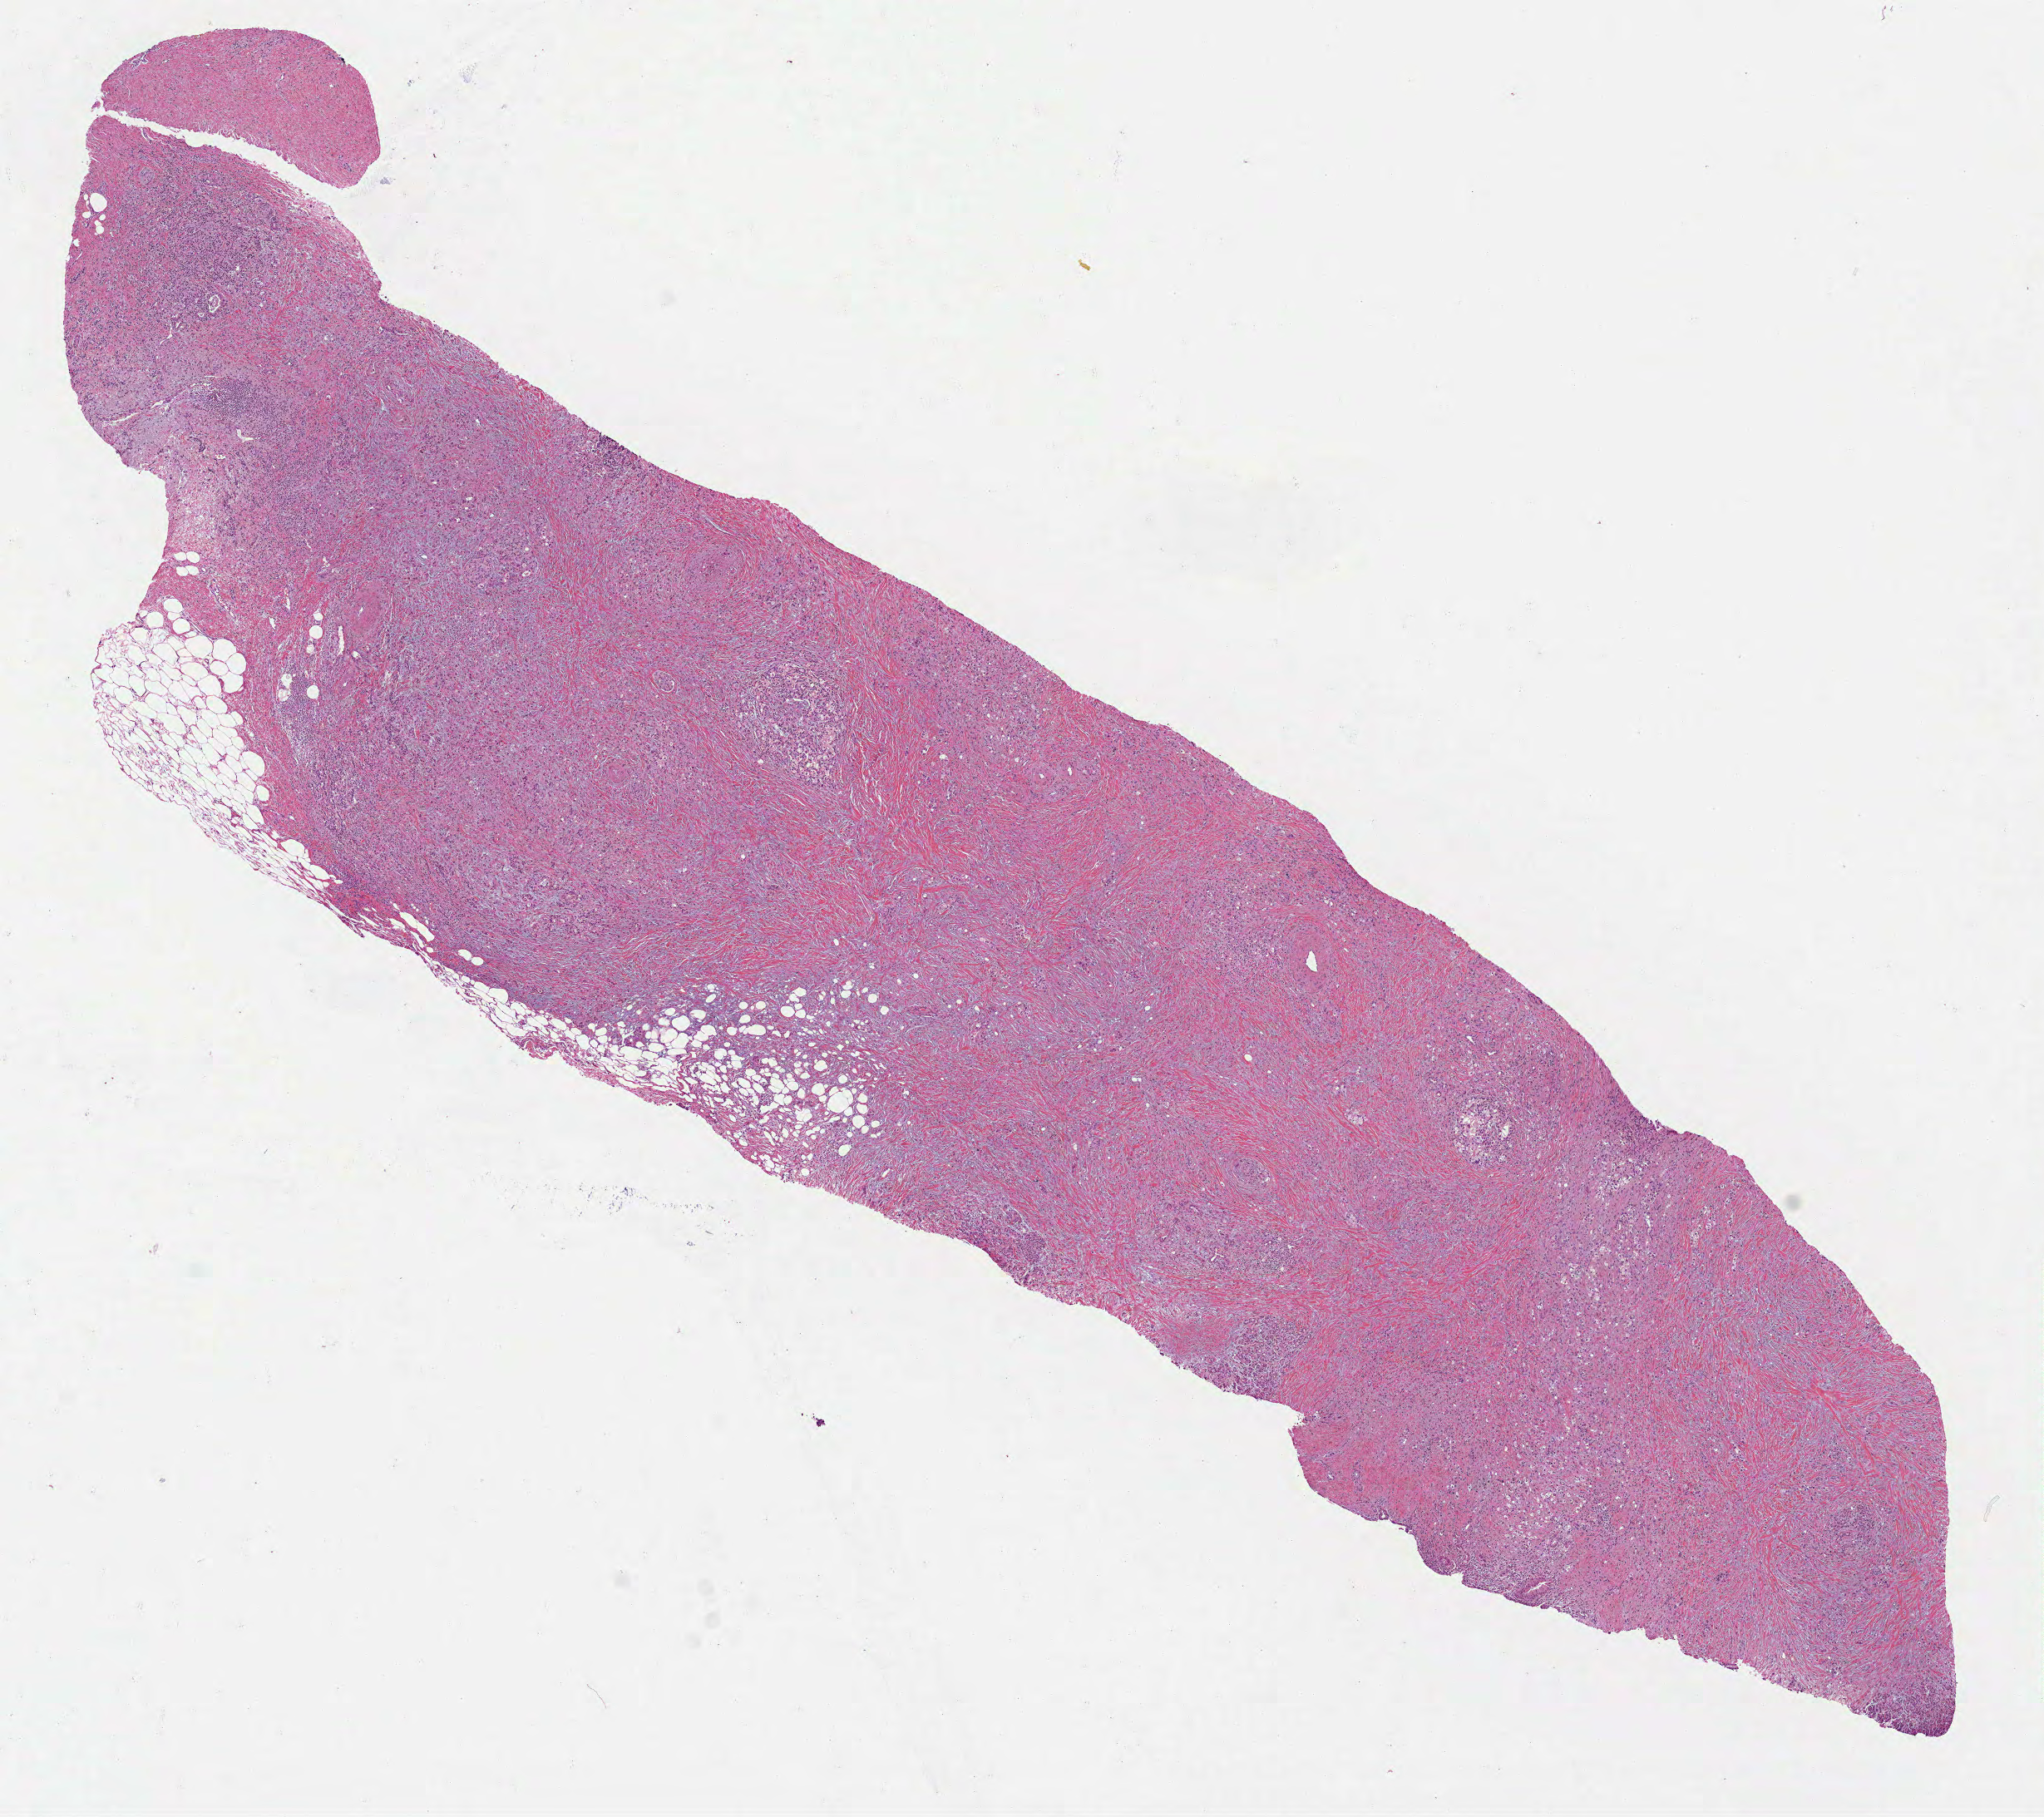
Hematoxylin and eosin (H&E) stained whole-slide image — a low-resolution overview of the entire scanned area, about 9.9 x 8.8 mm, FFPE section, primary tumour sample from the pancreas. Male, age 73 years at initial diagnosis. Histologic grade: G3 (poorly differentiated).
TNM: T1 N0 MX. AJCC pathologic stage: IA (7th edition). Histologic diagnosis: Adenocarcinoma, NOS (head of pancreas).